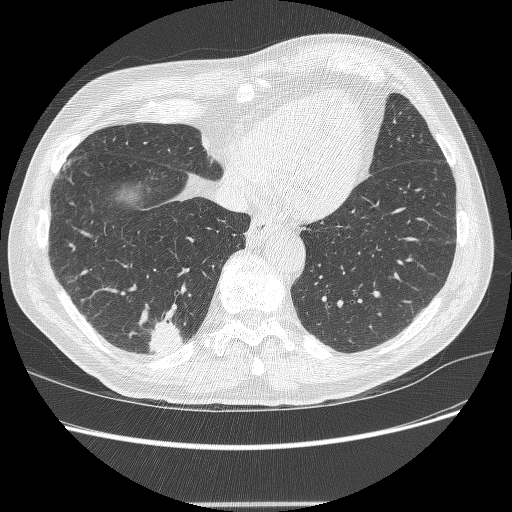
Chest CT (low-dose screening protocol), one axial image, second screening round (one year after baseline), lung window (W 1500 / L -600 HU), slice 65 of 245 in the series. Male, age 71 years at enrolment. Current smoker at enrolment.
Lesion marked by an expert reader, bounding box (x1, y1, x2, y2) in pixels: (137, 322, 188, 361). The screening reader recorded 5 non-calcified nodules or masses ≥4 mm on this exam (right lower lobe, right lower lobe, right upper lobe, right upper lobe, right upper lobe); which of them this box marks is not recorded. Participant outcome: lung cancer diagnosed 7 days after this screen — squamous cell carcinoma, NOS, right lower lobe, moderately differentiated (G2), stage IA (AJCC 6th edition), 27 mm at pathology.